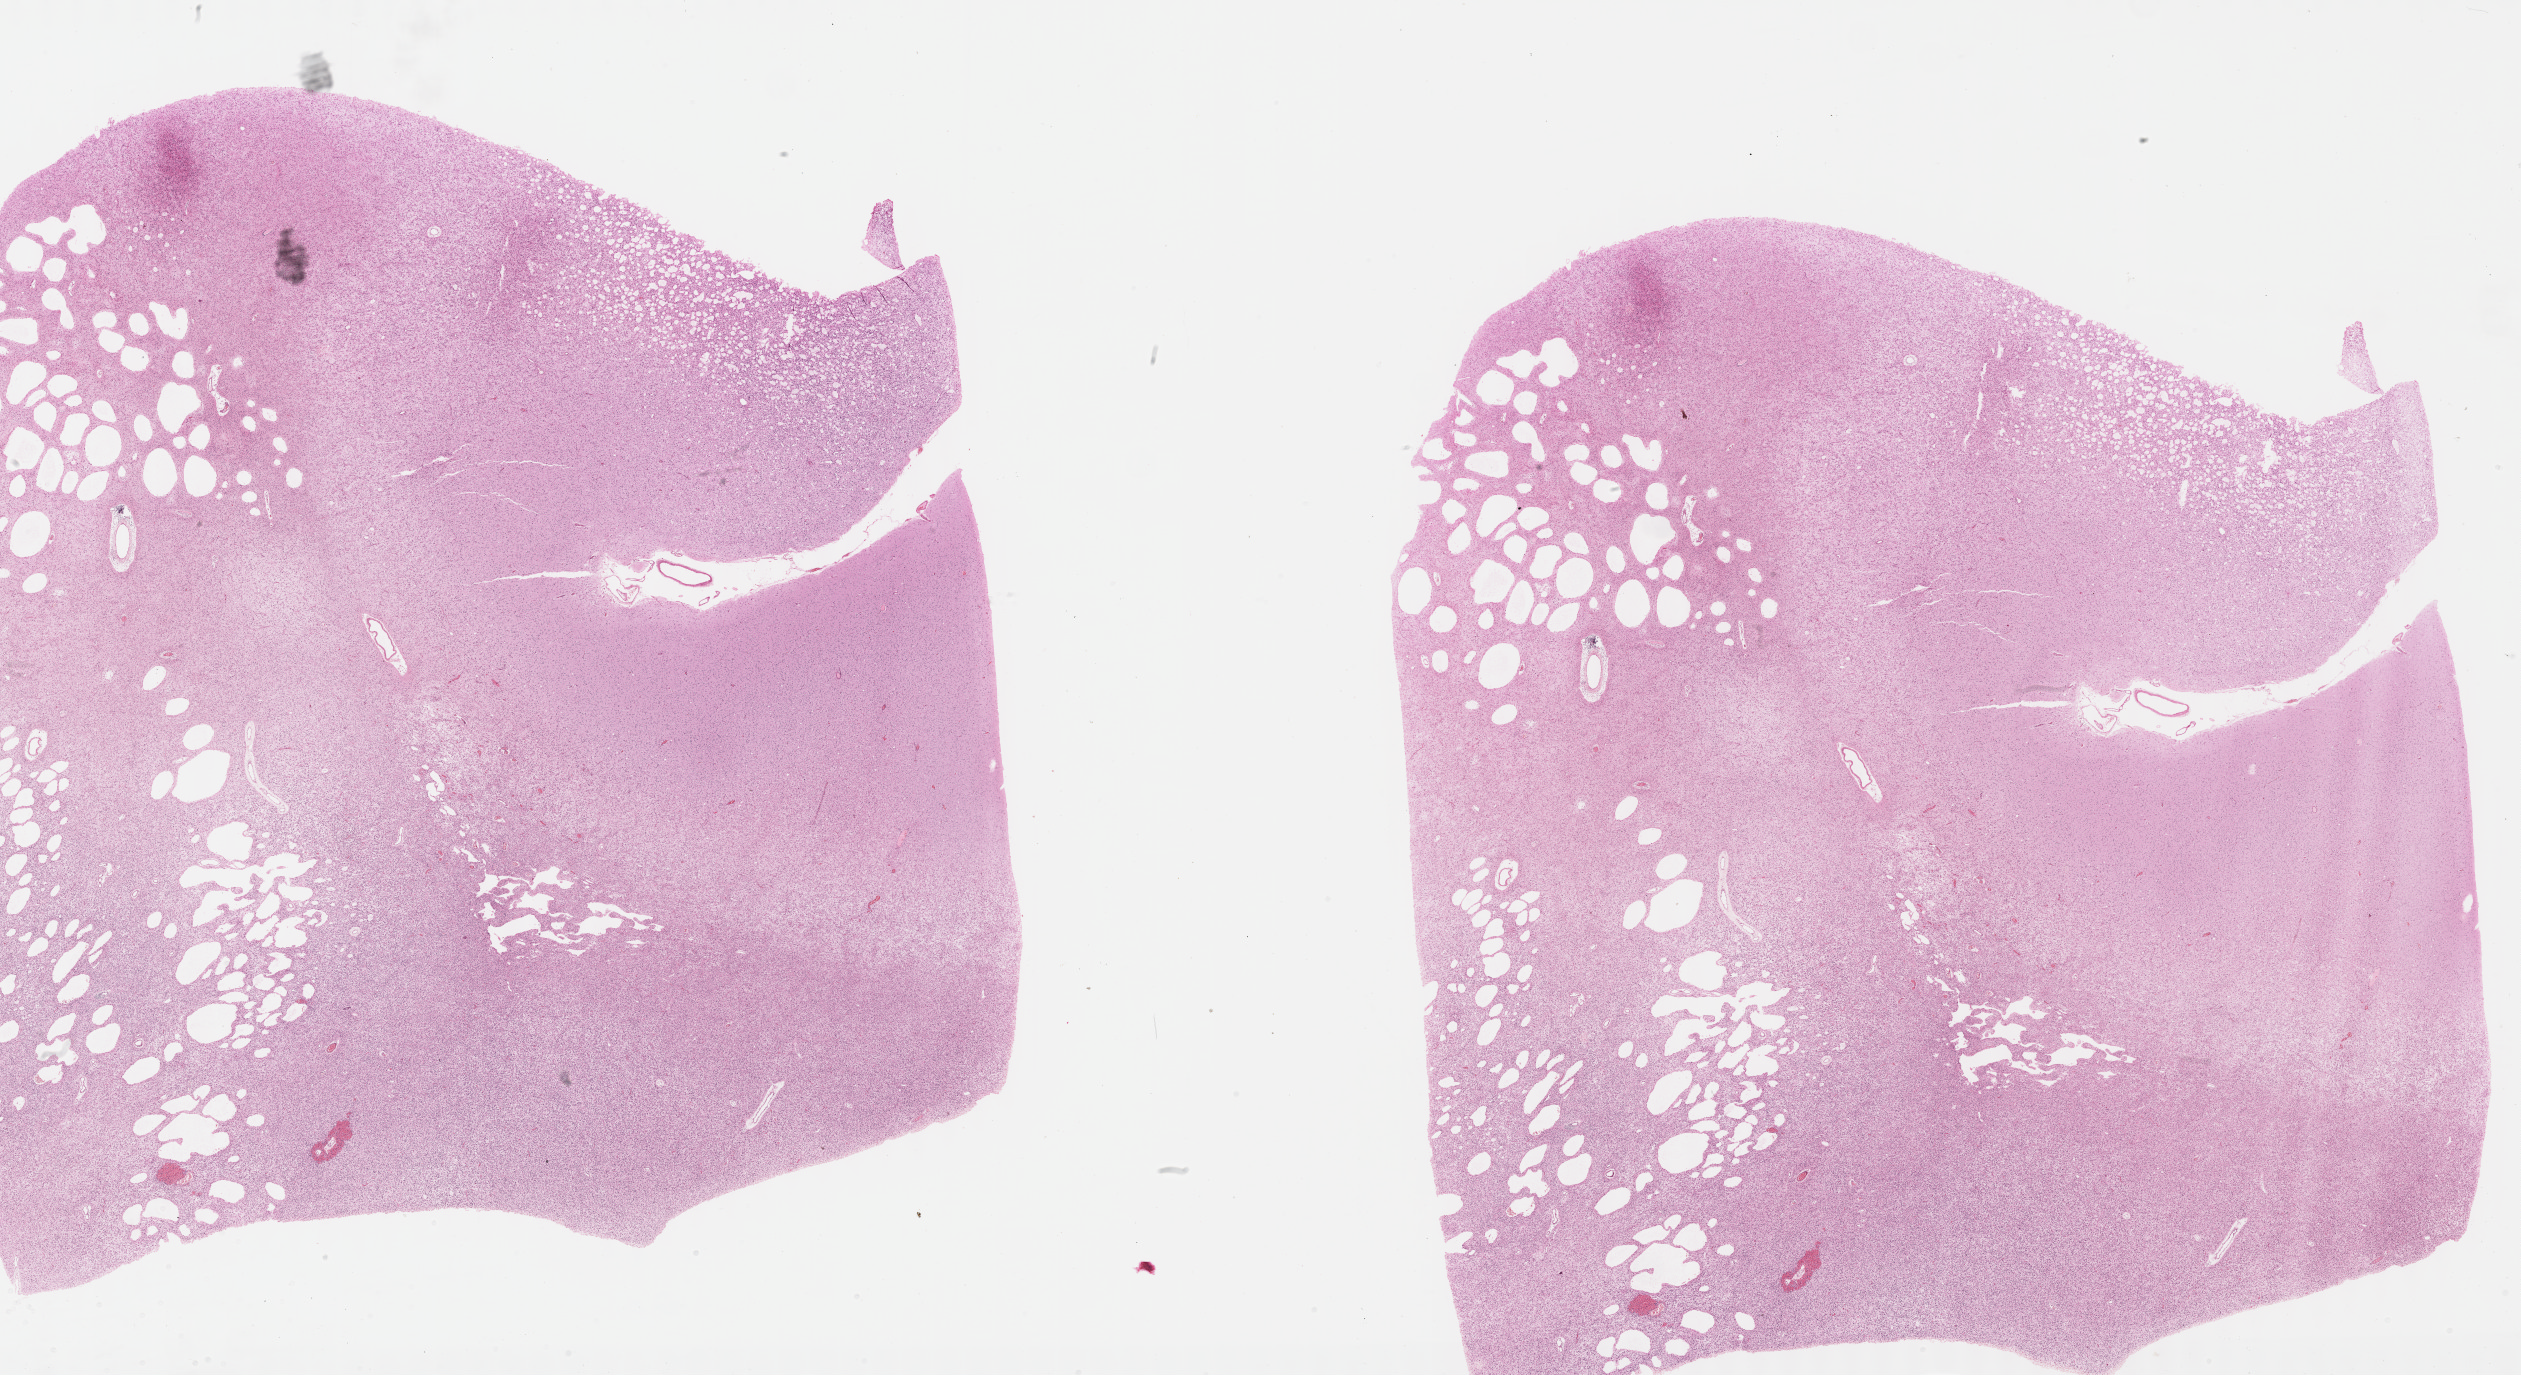
Digitized Hematoxylin and eosin (H&E) stained tissue section (whole slide), a low-resolution overview of the entire scanned area, about 40.7 x 22.2 mm (slide scanned at 40x). Formalin-fixed paraffin-embedded (FFPE) diagnostic section. Primary tumour sample from the brain. Male patient; age at initial diagnosis 29 years. Histologic grade: G2 (moderately differentiated).
* laterality: left
* histologic diagnosis: Oligodendroglioma, NOS (cerebrum)